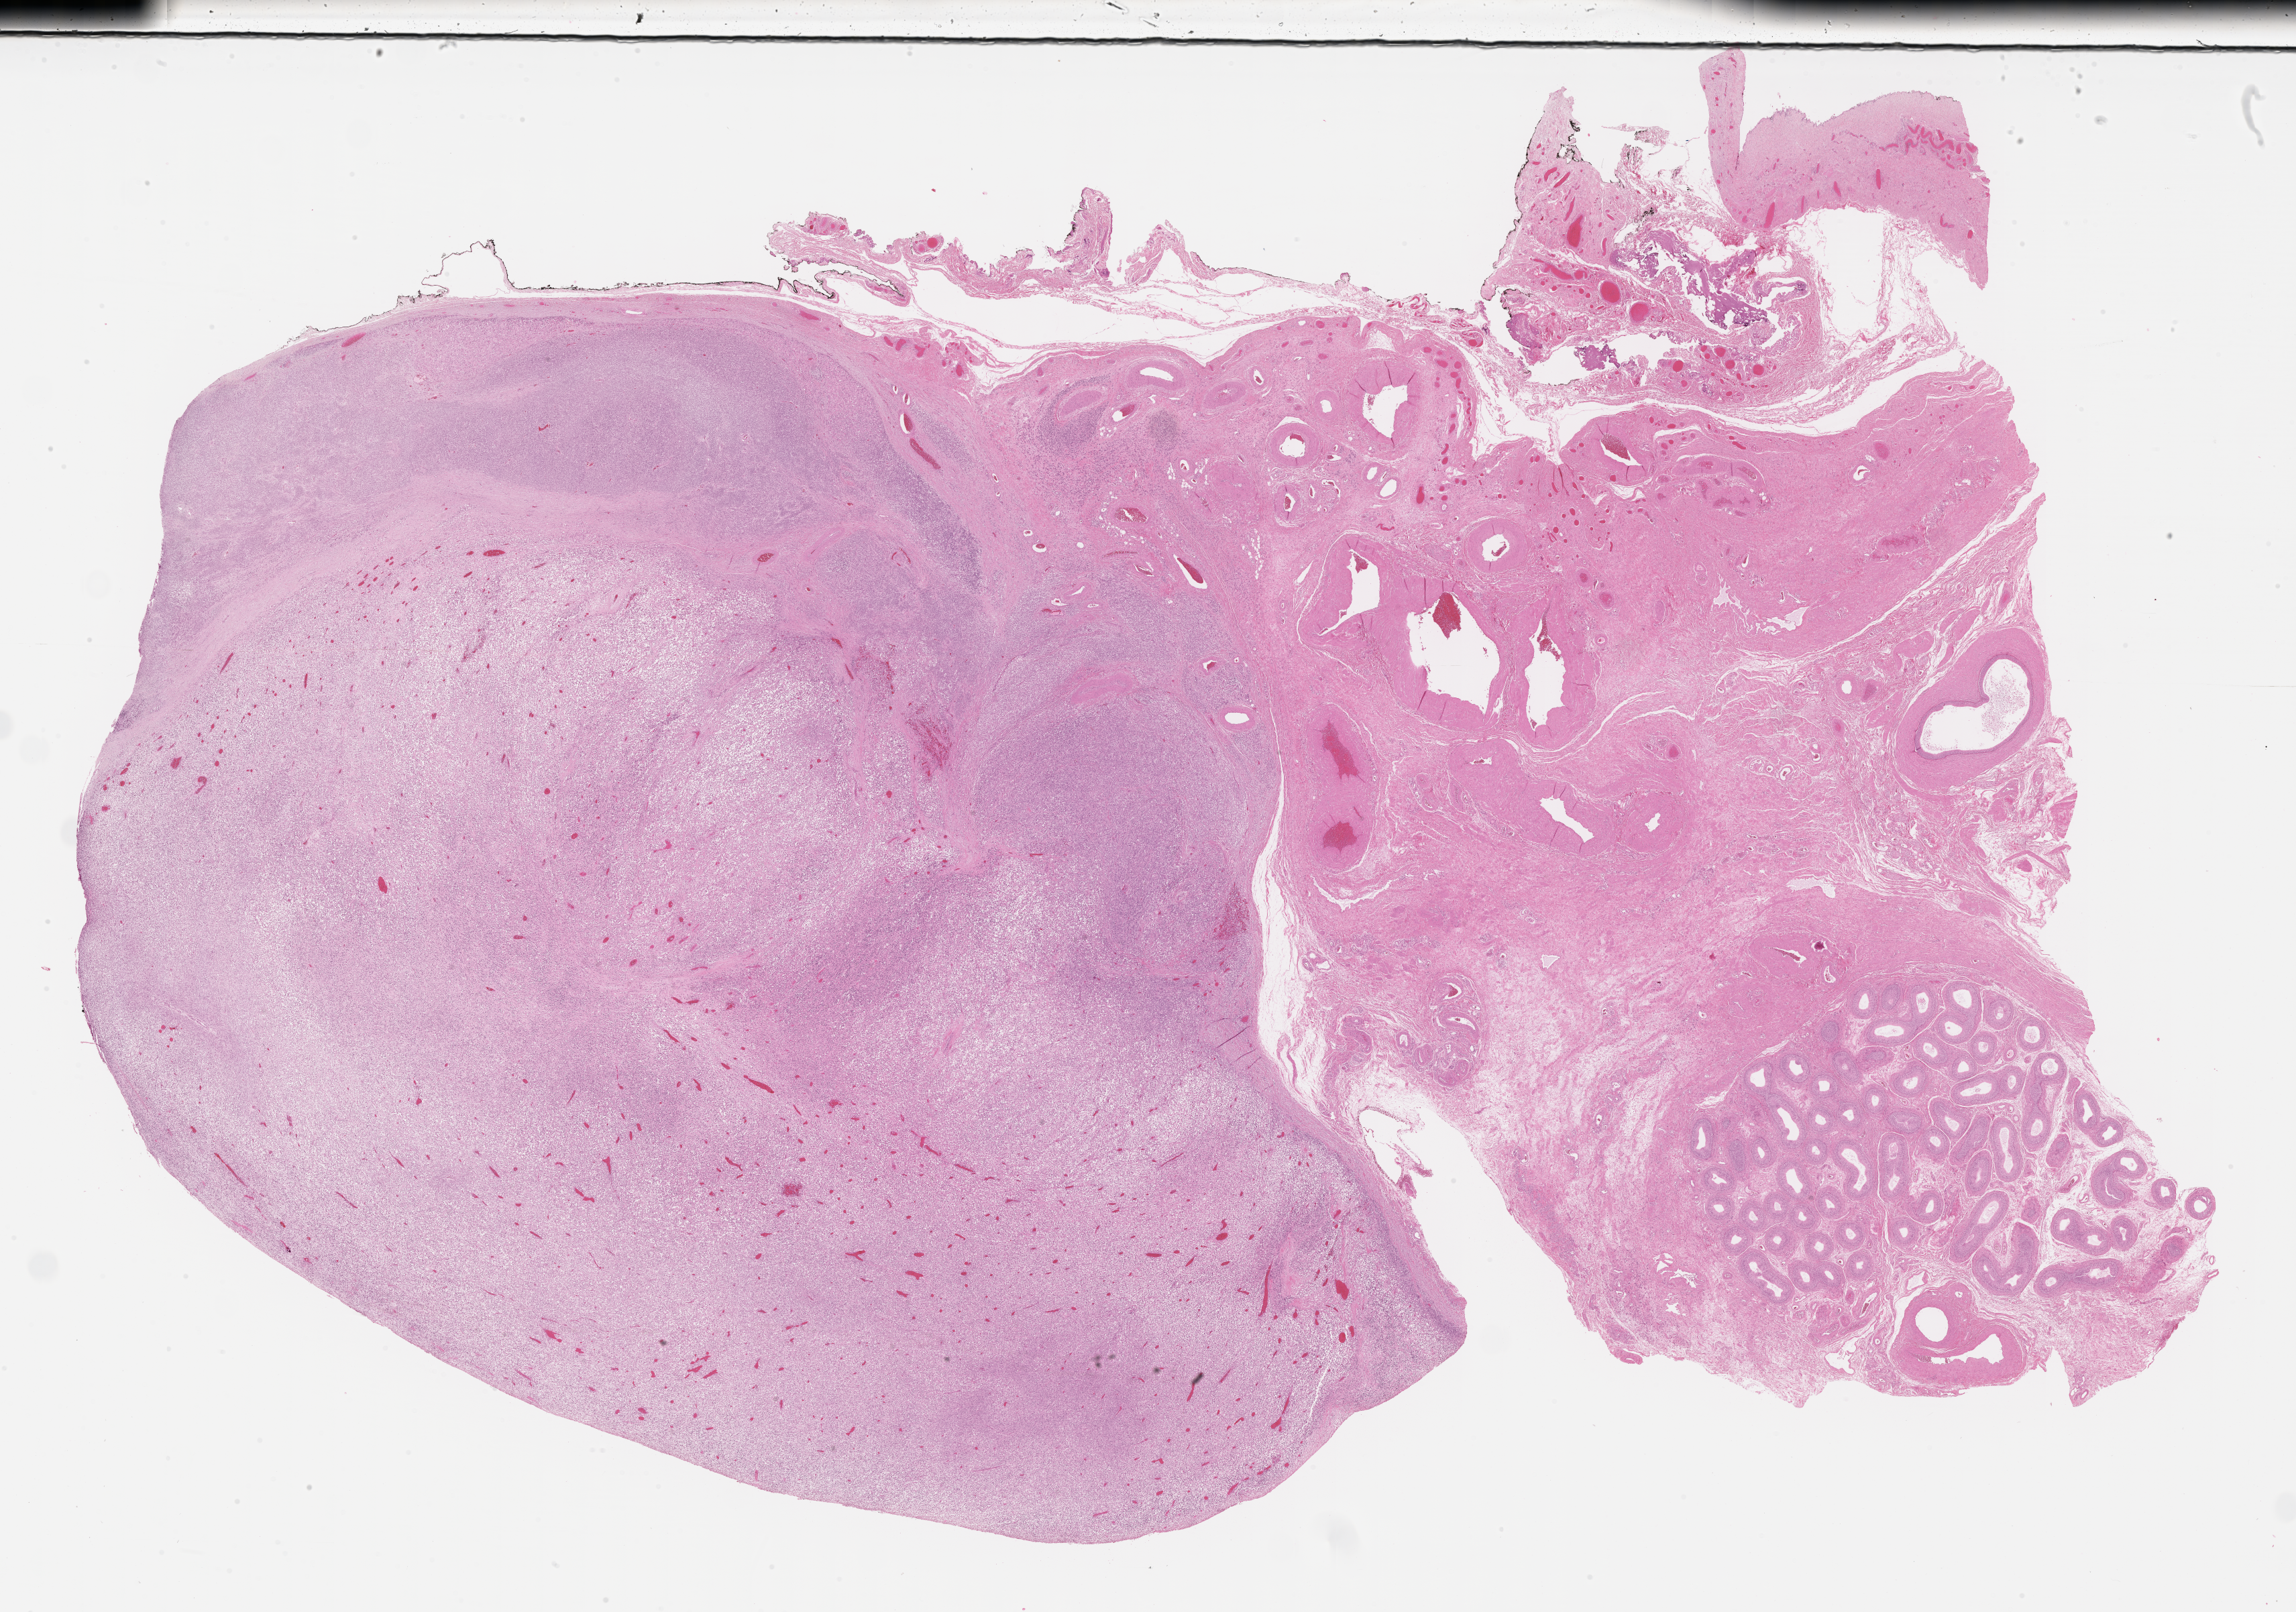
Haematoxylin and eosin whole-slide image of tumor tissue — low-resolution overview of the scanned area, about 27.7 x 19.4 mm, FFPE section, site: spermatic cord, left. Male patient, age at diagnosis 13.9 years.
Diagnosis: rhabdomyosarcoma; histological classification: embryonal rhabdomyosarcoma.